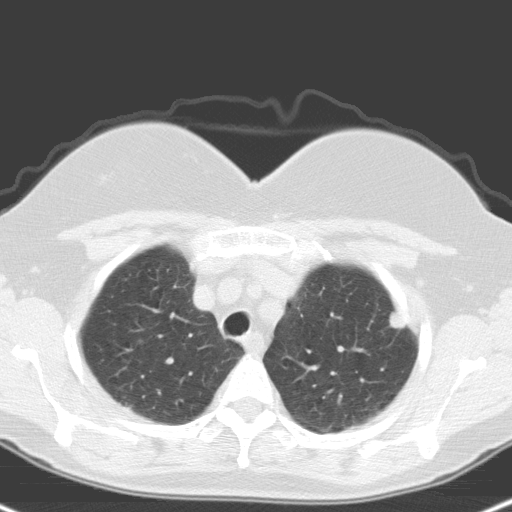
Low-dose screening chest CT, one axial slice. Position 127 of 148 along the scan axis. Lung window (W 1500 / L -600 HU). 512 × 512 image matrix, field of view 314 × 314 mm.
Annotated regions visible in this slice (manually delineated by an expert):
- lesion 1 (tumor, upper lobe of left lung): bounding box <389,311,409,330> (left, top, right, bottom; pixels)